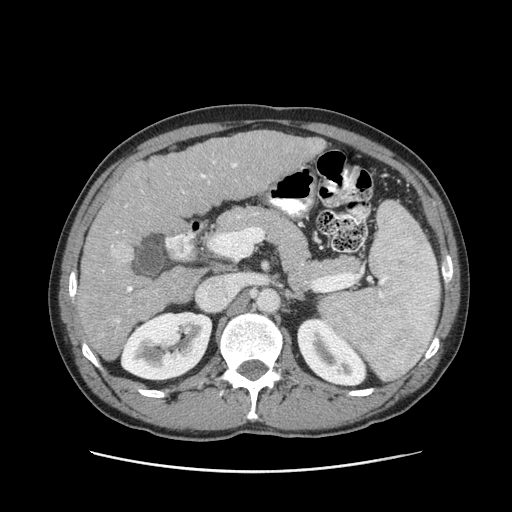
Contrast-enhanced abdominal CT (liver protocol), one axial slice. Slice 48 of 93 in the series (ordered by position). 120 kVp. Soft-tissue window (W 400 / L 40 HU). 2.5 mm slice thickness. 512 × 512 image matrix, field of view 380 × 380 mm. From the clinical record (not read from this slice): diagnosis: hepatocellular carcinoma (patient treated with transarterial chemoembolisation; whether this scan precedes or follows treatment is not stated here); TNM stage (as recorded): Stage-II; Child-Pugh class: A; tumour nodularity: multinodular; tumour size: 1 cm.
Annotated regions visible in this slice (semi-automatic segmentation, software-assisted and operator-edited):
- liver parenchyma outside the tumour (the mass and vessels are separate outlines, so this box may not span the whole liver): bounding box (x1, y1, x2, y2) in pixels: (76, 130, 325, 360)
- liver vessels: (111, 161, 237, 323)